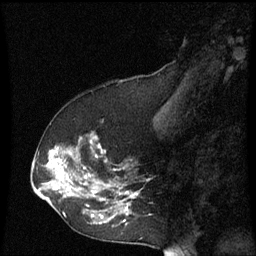
Breast MRI (dynamic contrast-enhanced), one sagittal slice. Position 25 of 60 along the scan axis. Dynamic contrast-enhanced series, image 2 of 3 at this slice position (ordered by acquisition). 1.5 T. TE 4.2 ms, TR 8.9 ms. 2 mm slice thickness. 256 × 256 image matrix, field of view 200 × 200 mm. Patient: female, 53 years. Case-level facts recorded for this patient, not image findings: setting: breast cancer imaged before/during neoadjuvant chemotherapy; receptor status: HR-positive, HER2-negative.
Structures marked on this image (semi-automatically segmented with operator editing):
- analysis volume of interest (the breast-tissue region the enhancement analysis was run in; not a lesion): bounding box <38,134,151,229> (left, top, right, bottom; pixels)
- tumour enhancement mask (voxels above the 70 % enhancement threshold inside the analysis volume of interest): <48,138,139,223>